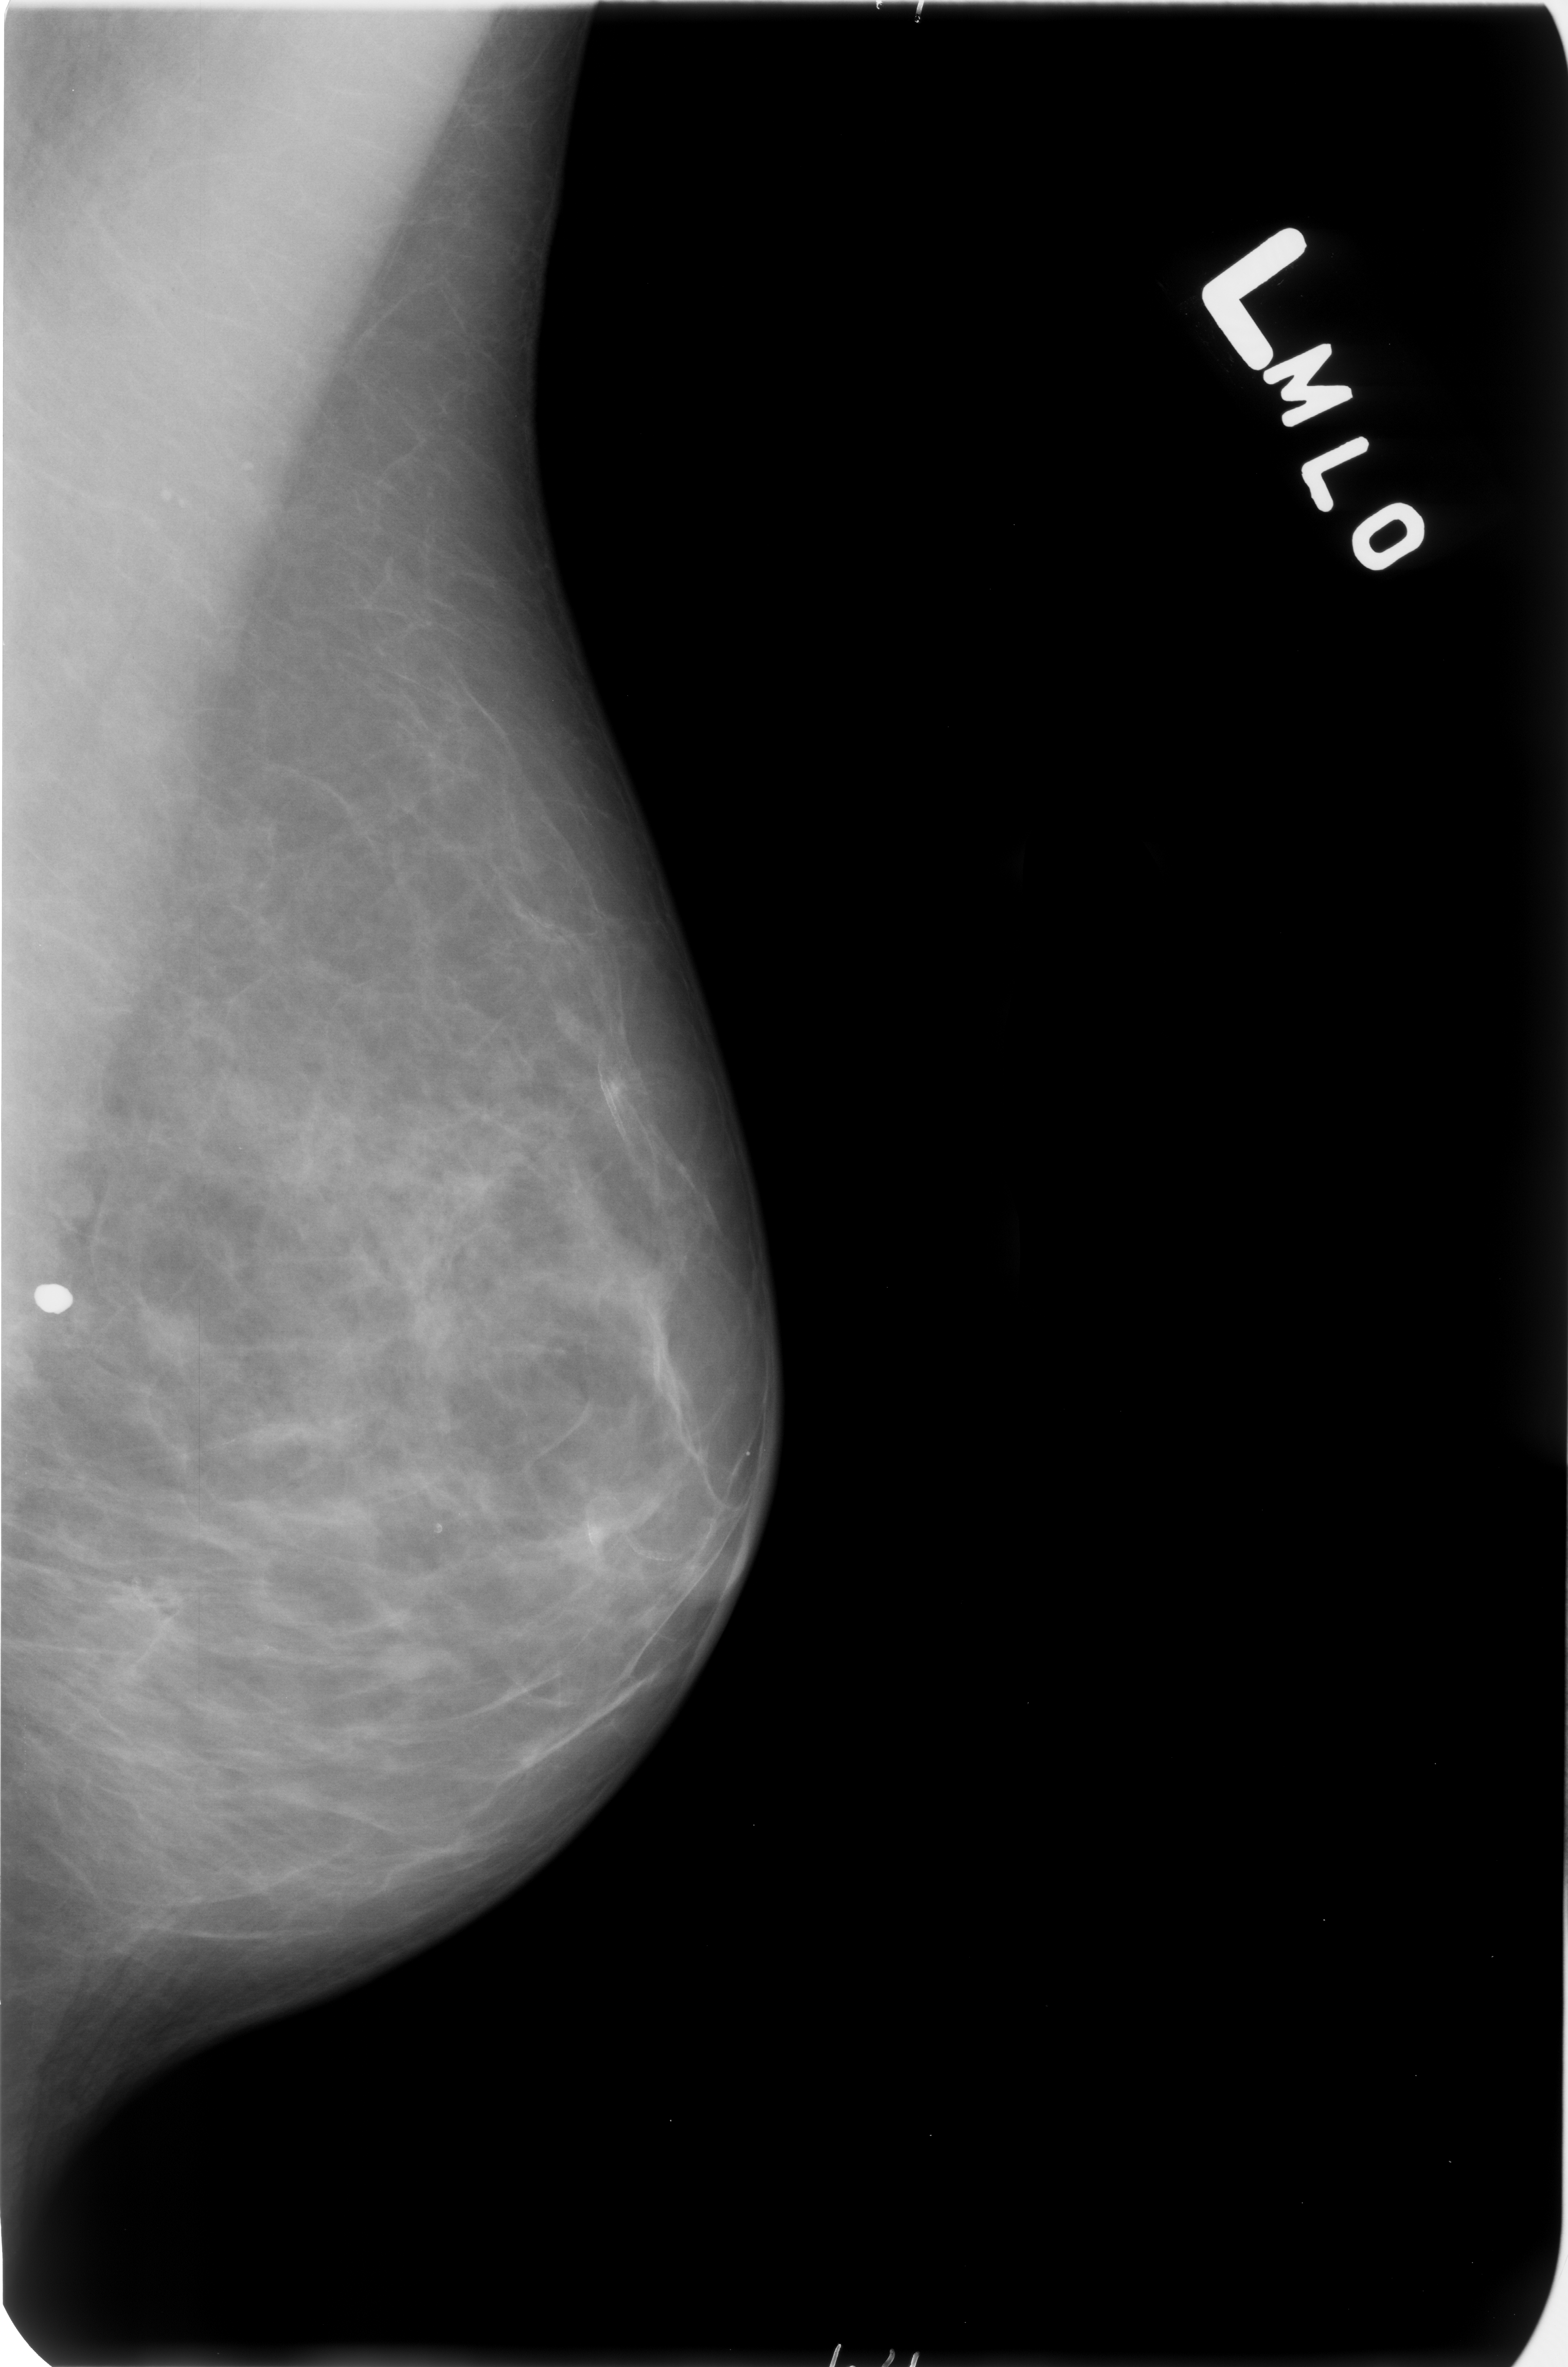
Mammogram (digitized film). Left breast. Mediolateral oblique (MLO) view. Breast composition: scattered fibroglandular densities (BI-RADS density category 2 of 4). 1568 × 2367 image matrix.
Expert-marked regions of interest on this image (one box per marked abnormality):
- Finding 1 of 2: calcifications, morphology coarse; BI-RADS assessment category 2; subtlety rating 5 on a 1 (subtle) to 5 (obvious) scale; outcome (as recorded, no biopsy): benign without callback (not worked up further): box from (x=28, y=1263) to (x=79, y=1322) px
- Finding 2 of 2: calcifications, morphology vascular; BI-RADS assessment category 2; benign; no additional work-up was recommended (outcome (as recorded, no biopsy): benign without callback): (x=485, y=864)–(x=701, y=1220)